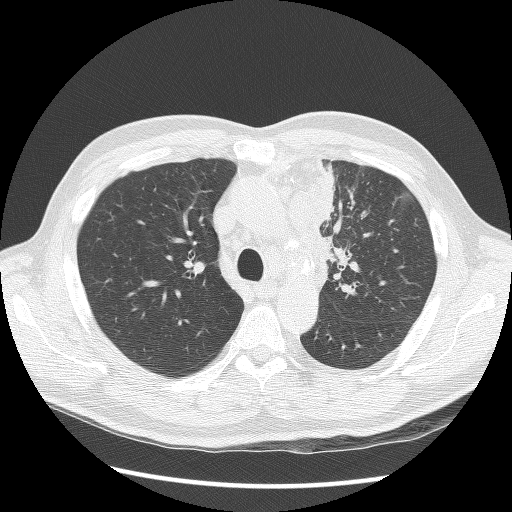
Low-dose screening chest CT, axial slice; second annual screen; lung window (W 1500 / L -600 HU); 512 × 512 image matrix, field of view 360 × 360 mm. Male participant, aged 64 years at enrolment. Former smoker at enrolment.
- Lesion marked by an expert reader, box from (x=297, y=168) to (x=368, y=290) px.
- Screening reader's record for this exam: no non-calcified nodule ≥4 mm recorded.
- Lung cancer was diagnosed 24 days after this screen: small cell carcinoma, NOS, left upper lobe, stage IV (AJCC 6th edition), 100 mm at pathology.